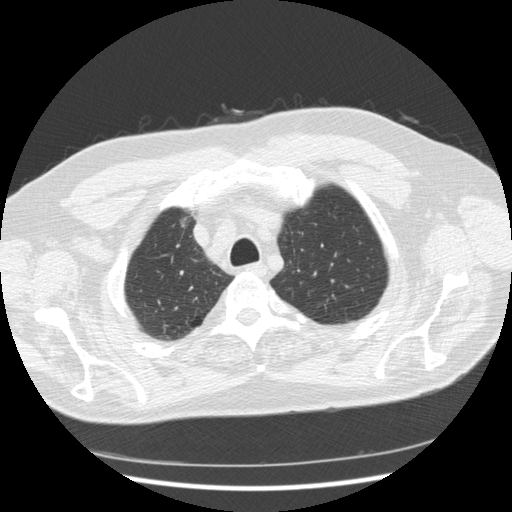
Low-dose screening chest CT, axial slice. Second screening round (one year after baseline). Lung window (W 1500 / L -600 HU). 2.5 mm slice thickness. Slice 38 of 267 in the series. Male participant, aged 66 years at enrolment. Former smoker at enrolment.
• Expert-annotated lung lesion, bounding box <155,204,204,243> (left, top, right, bottom; pixels).
• No non-calcified nodule or mass ≥4 mm was recorded by the screening reader at this exam.
• Later outcome: lung cancer diagnosed 603 days after this screen (after the third annual screen) — bronchiolo-alveolar adenocarcinoma, NOS, right upper lobe, moderately differentiated (G2), stage IA (AJCC 6th edition), 12 mm at pathology.